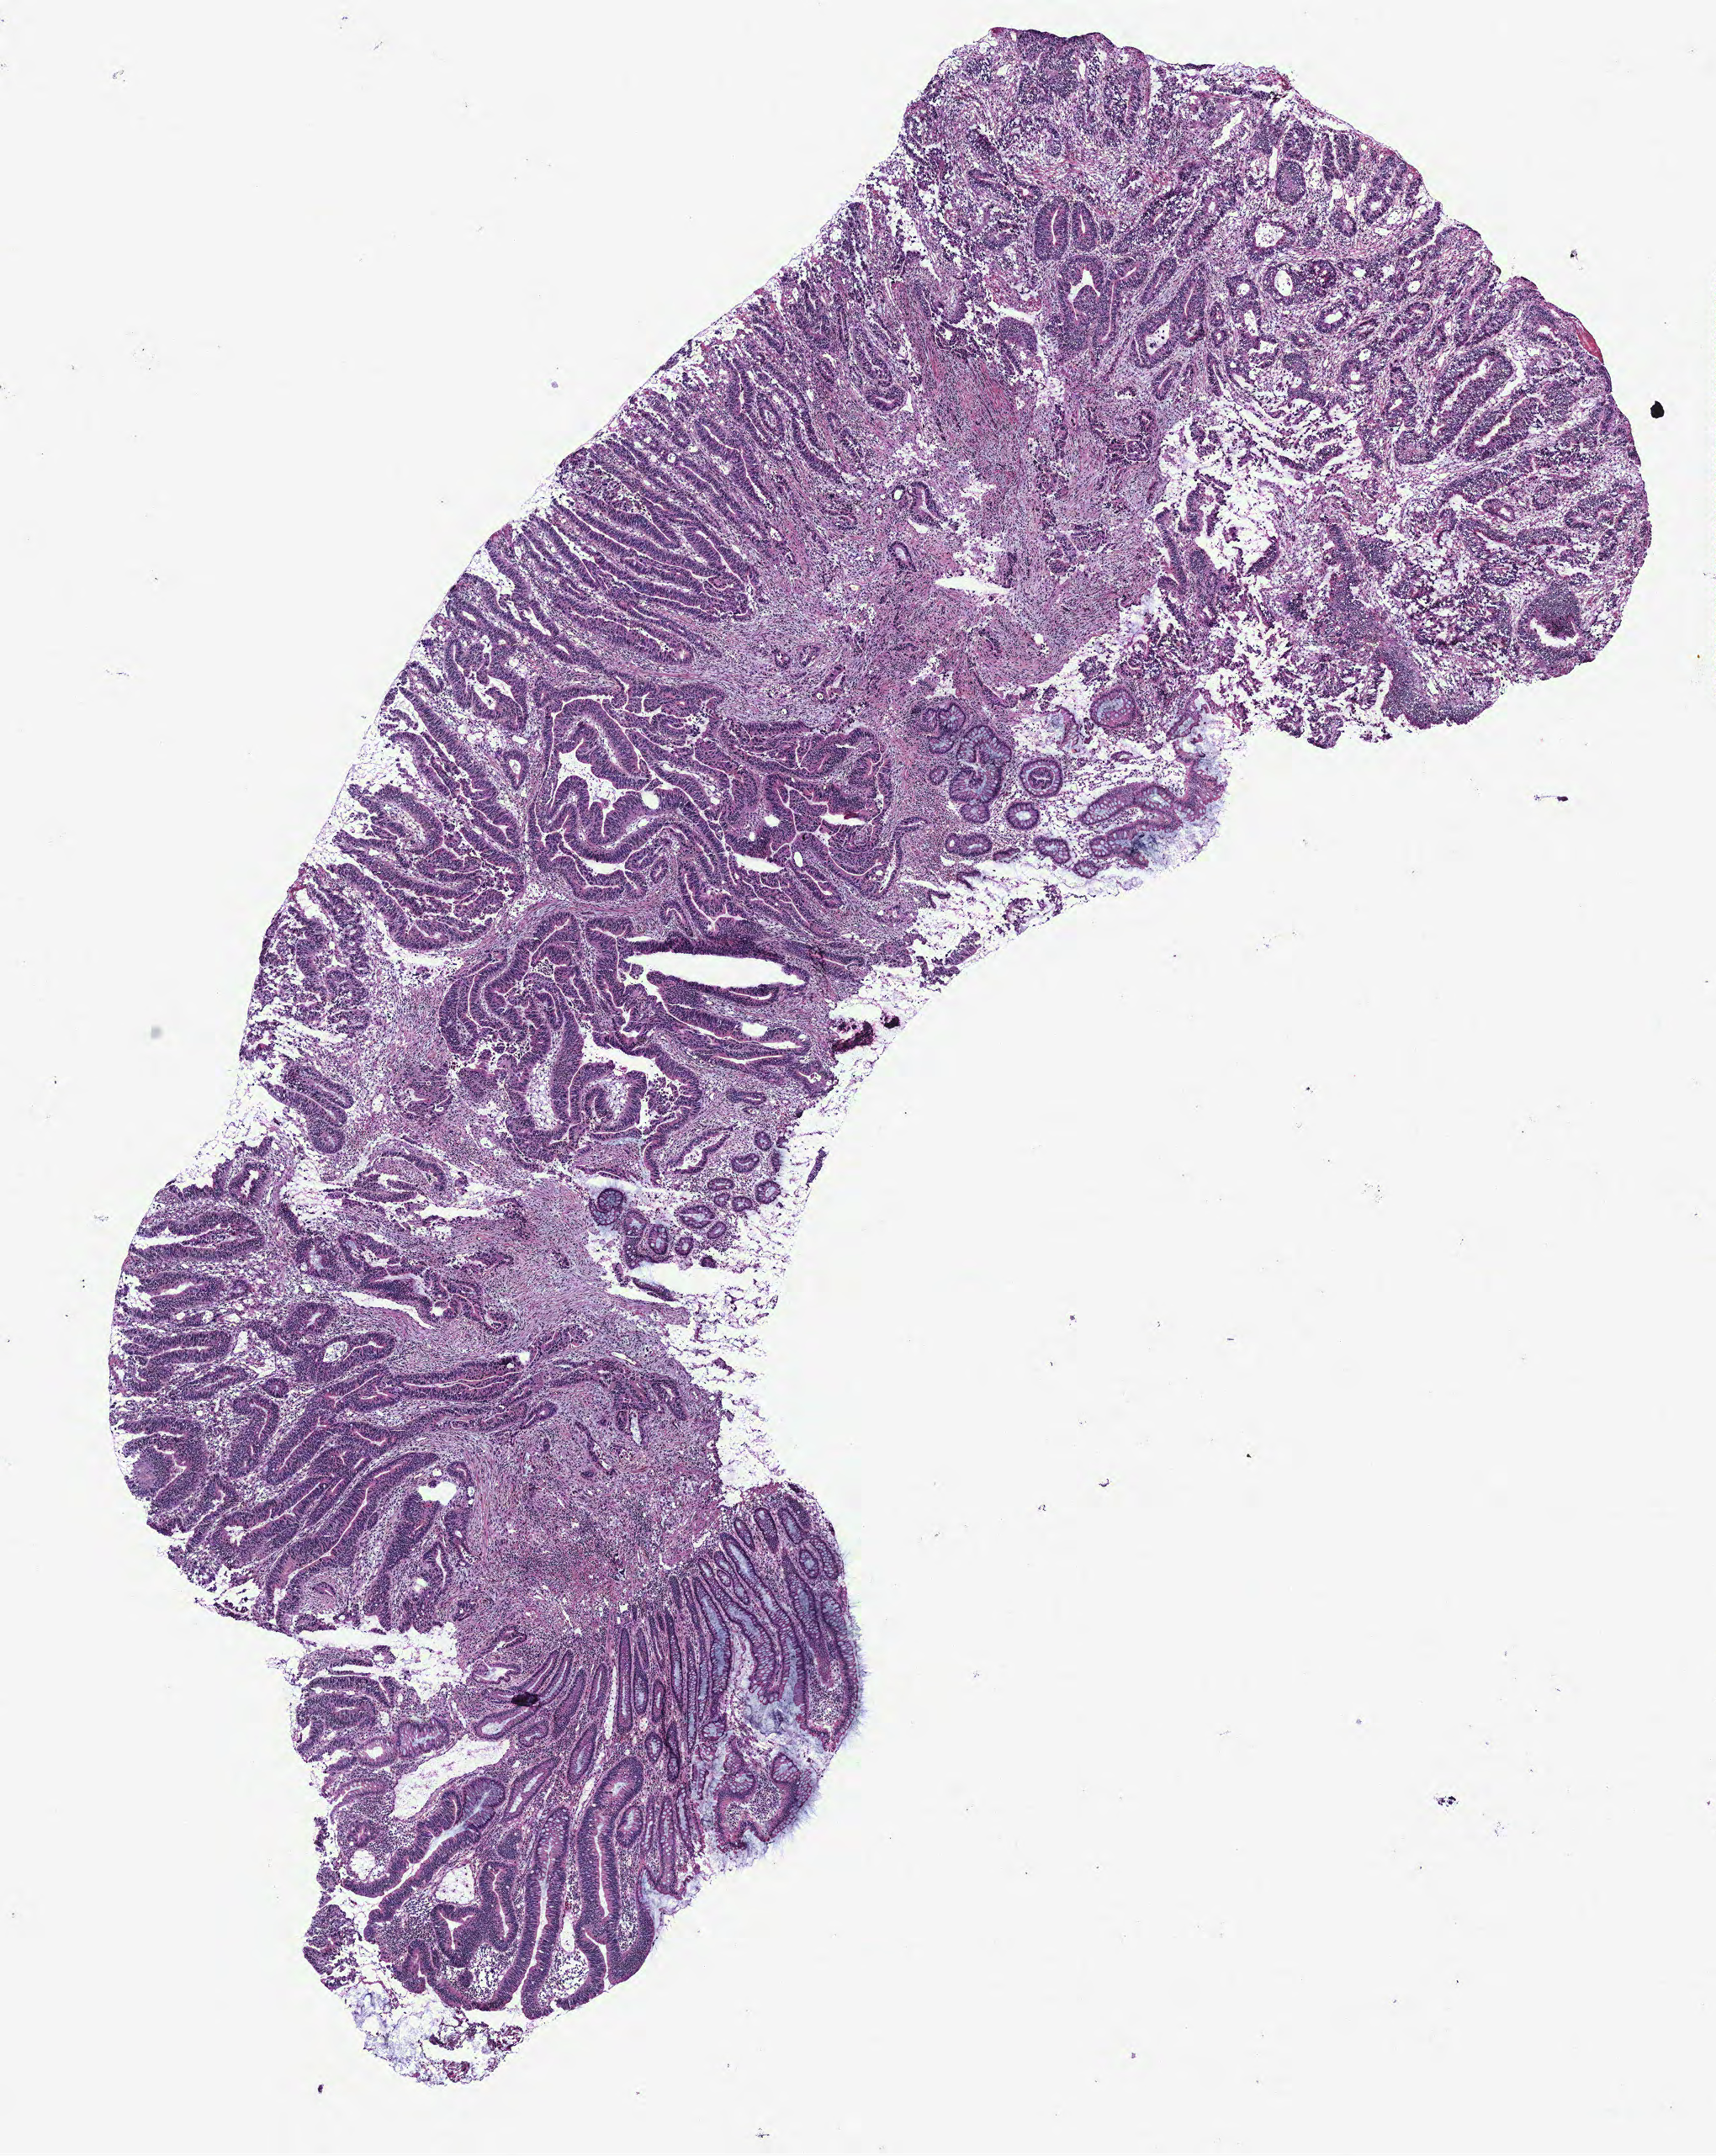
Hematoxylin and eosin (H&E) stained whole-slide image — whole scanned area (about 8.2 x 10.3 mm, from a 40x scan) shown as a low-resolution overview, colon, normal (non-tumour) tissue. Male, 57 y/o.
• this section: normal (non-tumour) tissue from the same patient
• patient diagnosis: Adenocarcinoma, NOS